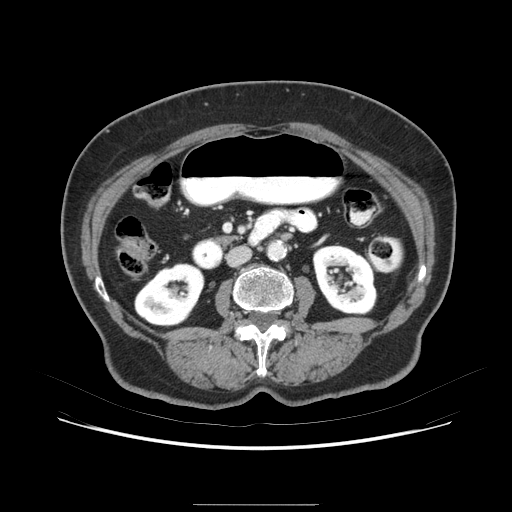
Contrast-enhanced abdominal CT (liver protocol), one axial slice. Position 16 of 79 along the scan axis. 120 kVp. Soft-tissue window (W 400 / L 40 HU). 512 × 512 image matrix. Case-level facts recorded for this patient, not image findings: diagnosis: hepatocellular carcinoma (patient treated with transarterial chemoembolisation; whether this scan precedes or follows treatment is not stated here); TNM stage (as recorded): Stage-I; Child-Pugh class: A.
Structures marked on this image (semi-automatically segmented with operator editing):
- liver parenchyma outside the tumour (the mass and vessels are separate outlines, so this box may not span the whole liver): box from (x=102, y=206) to (x=116, y=250) px